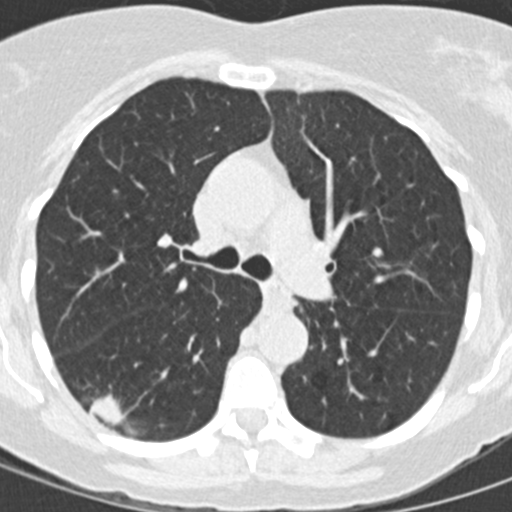
Low-dose screening chest CT, one axial slice. Position 92 of 146 along the scan axis. 120 kVp. Lung window (W 1500 / L -600 HU). 2 mm slice thickness. 512 × 512 image matrix, field of view 270 × 270 mm.
Outlined on this slice (expert manual segmentation):
- lesion 1 (tumor, lower lobe of right lung): bounding box [x1, y1, x2, y2] px = [89, 394, 126, 424]